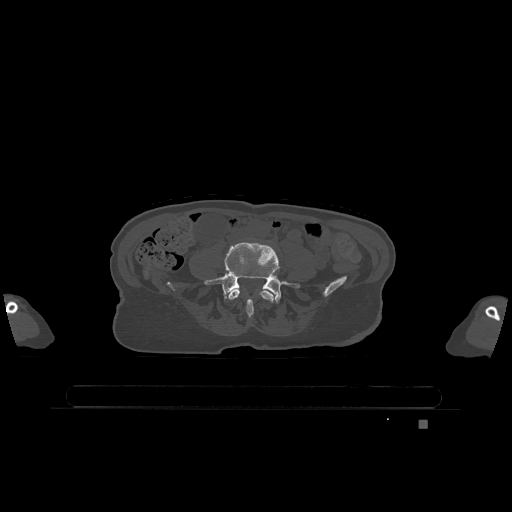
CT including the spine, one axial slice; slice 260 of 1317 in the series (ordered by position); bone window (W 1800 / L 400 HU); 0.5 mm slice thickness; 512 × 512 image matrix, field of view 500 × 500 mm. Patient: female, 74 years. From the clinical record (not read from this slice): primary cancer: lung; vertebrae with lytic lesions (as recorded): T1, T4, T5, T6, L4, L5.
Structures marked on this image (semi-automatic segmentation, software-assisted and operator-edited):
- L4 vertebra: bounding box <227,289,274,318> (left, top, right, bottom; pixels)
- L5 vertebra: <204,242,300,304>